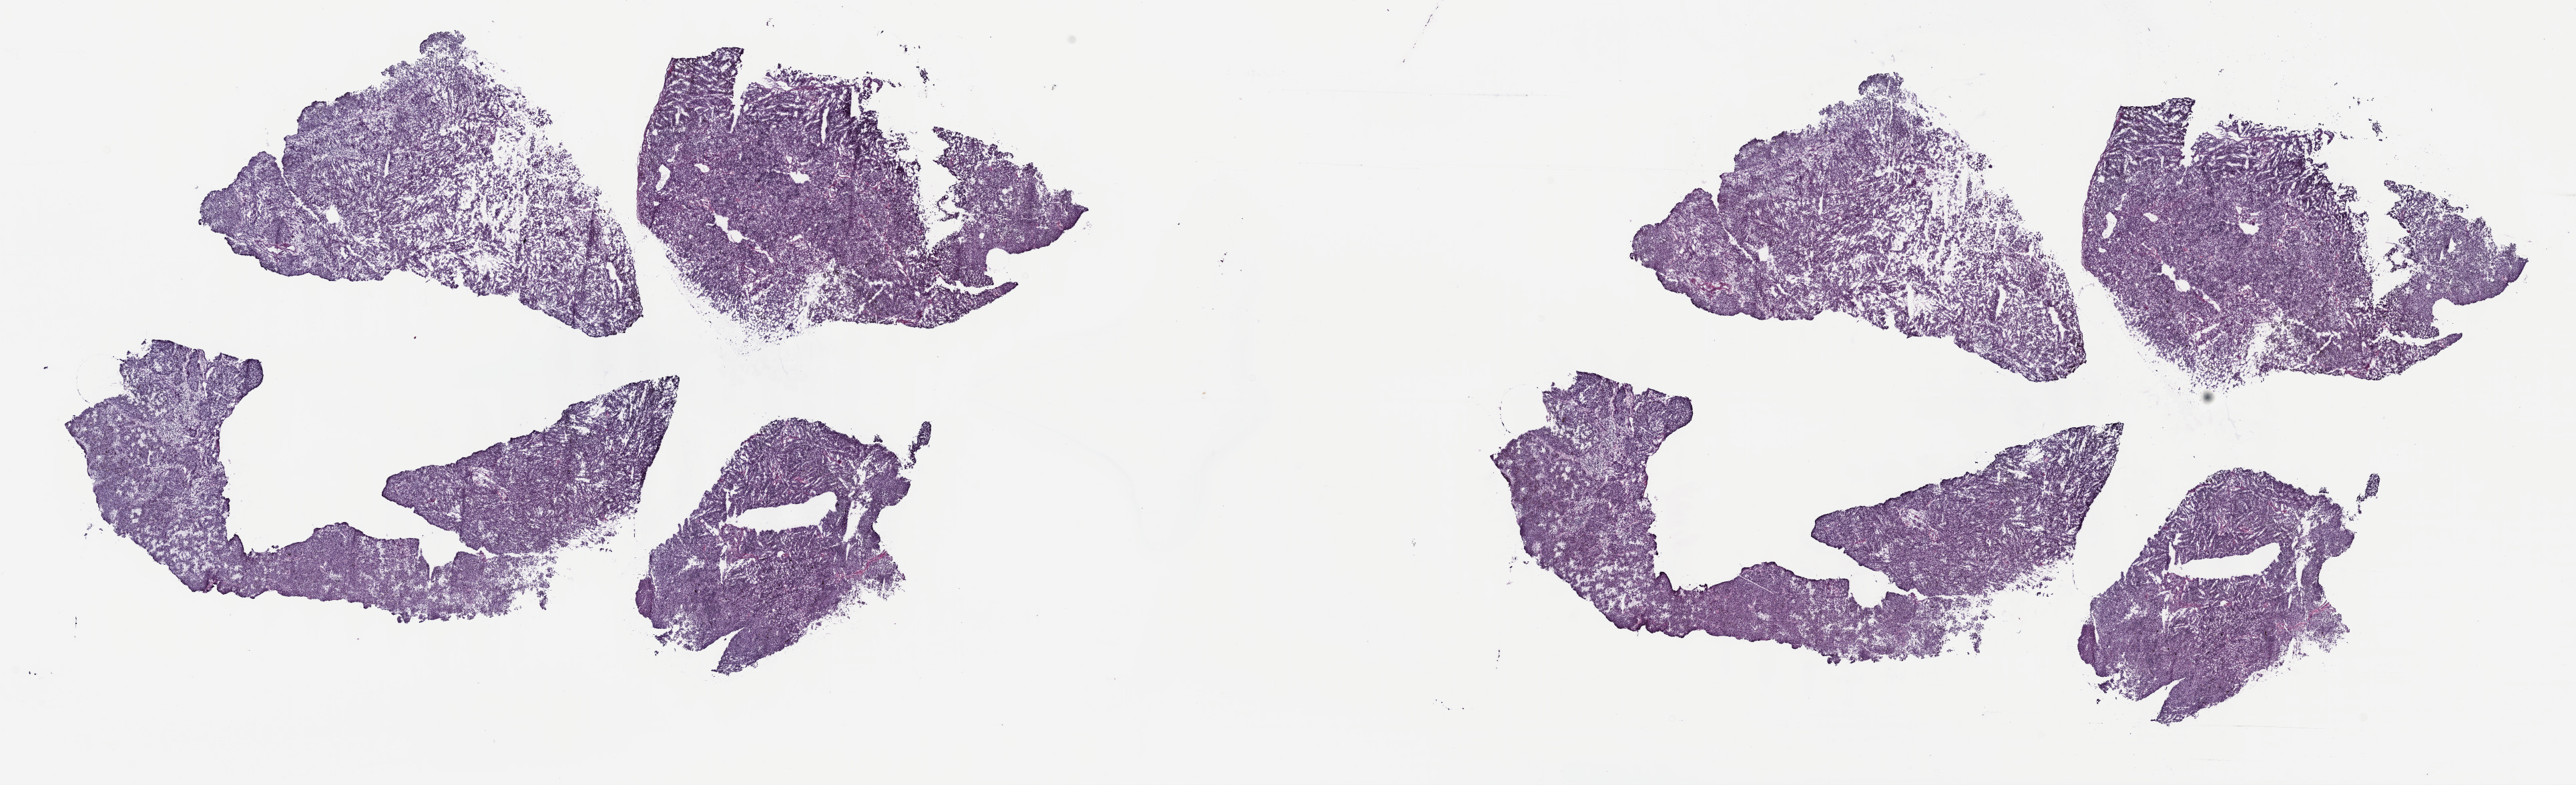
Digitized Hematoxylin and eosin (H&E) stained tissue section (whole slide) — shown as a low-resolution overview of the whole scanned area (about 31.2 x 9.5 mm), frozen section from the top of the tissue portion, primary tumour sample from the uvea. Female, age 59 years at initial diagnosis. Composition of this section per pathologist review: tumour cells 100%, tumour nuclei 80%, normal cells 0%, stromal cells 0%, necrosis 0%. Infiltration values recorded for this section: lymphocyte infiltration 1%, monocyte infiltration 0%, neutrophil infiltration 0%.
* laterality: right
* AJCC pathologic stage: IIIA (7th edition)
* diagnosis: Mixed epithelioid and spindle cell melanoma (choroid)
* TNM: T4a N0 M0